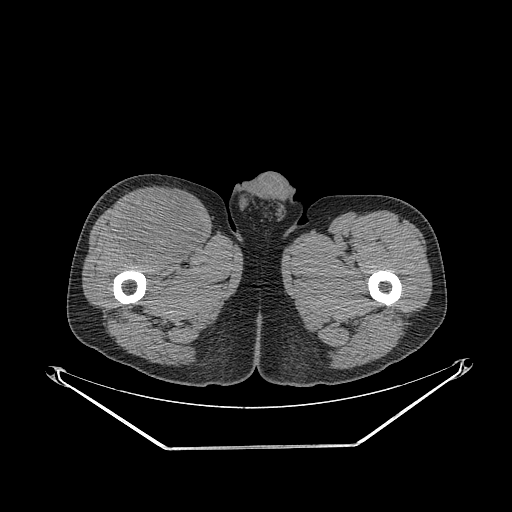
CT of an extremity soft-tissue mass (from a PET/CT study), one axial slice; position 292 of 311 along the scan axis; 140 kVp; soft-tissue window (W 400 / L 40 HU); 3.75 mm slice thickness; 512 × 512 image matrix, field of view 500 × 500 mm. Male patient. Case-level facts recorded for this patient, not image findings: histological type: pleiomorphic leiomyosarcoma; grade: intermediate; site of the primary tumour: right thigh.
Annotated regions visible in this slice (expert contour drawn on MRI and transferred to this co-registered scan by the dataset authors):
- gross tumour volume including surrounding oedema: bounding box [x1, y1, x2, y2] px = [116, 192, 204, 264]
- gross tumour volume (mass): [117, 192, 204, 264]